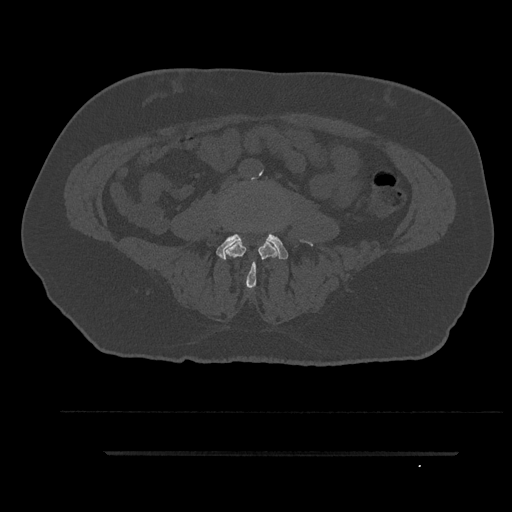
CT including the spine, one axial slice; position 4 of 797 along the scan axis; reconstruction kernel Br40s/3; bone window (W 1800 / L 400 HU); 512 × 512 image matrix, field of view 432 × 432 mm. Patient: male, 63 years. Case-level facts recorded for this patient, not image findings: primary cancer: renal; vertebrae with lytic lesions (as recorded): T8.
Outlined on this slice (semi-automatically segmented with operator editing):
- L3 vertebra: bounding box [x1, y1, x2, y2] px = [225, 240, 278, 288]
- L4 vertebra: [216, 234, 288, 260]